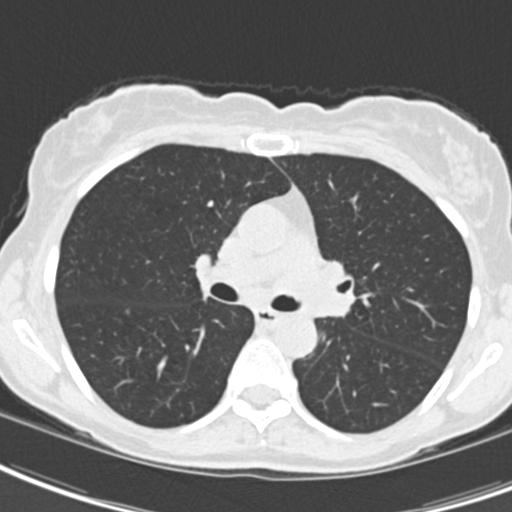
Chest CT (low-dose screening protocol), one axial image; first (baseline) screen; lung window (W 1500 / L -600 HU); standard (soft-tissue) reconstruction kernel (B30f); 120 kVp; slice 67 of 189 in the series. Female participant, aged 62 years at enrolment. Current smoker at enrolment.
Expert-annotated lung lesion, bounding box <296,246,372,329> (left, top, right, bottom; pixels). The exam's reader record, not a measurement of the box and not confirmed to be the same lesion: non-calcified nodule or mass ≥4 mm, right upper lobe, 24 × 20 mm, smooth margins, ground glass attenuation. Note: the box lies in the patient's left hemithorax on this image, whereas the reader's record names the right lung; they may be different findings. Official screen result: positive, change unspecified: nodule(s) >= 4 mm or enlarging nodule(s), mass(es), or other non-specific abnormalities suspicious for lung cancer. Participant outcome: lung cancer diagnosed 24 days after this screen — oat cell carcinoma, left hilum, left main stem bronchus, stage IIIB (AJCC 6th edition), 50 mm at pathology.